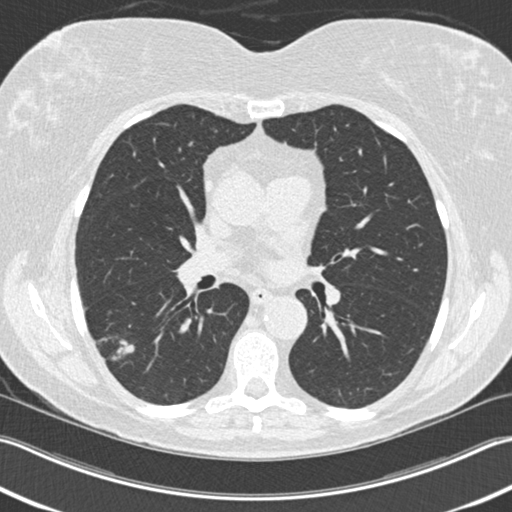
Low-dose screening chest CT, axial slice, baseline annual screen, lung window (W 1500 / L -600 HU), 2 mm slice thickness. Female participant, aged 63 years at enrolment.
- Lesion marked by an expert reader, bounding box <89,322,147,372> (left, top, right, bottom; pixels).
- The screening reader recorded 3 non-calcified nodules or masses ≥4 mm on this exam (right upper lobe, right lower lobe, right lower lobe); which of them this box marks is not recorded.
- Official screen result: positive, change unspecified: nodule(s) >= 4 mm or enlarging nodule(s), mass(es), or other non-specific abnormalities suspicious for lung cancer.
- Participant outcome: lung cancer diagnosed 57 days after this screen — bronchiolo-alveolar adenocarcinoma, NOS, right lower lobe, well differentiated (G1), stage IA (AJCC 6th edition), 25 mm at pathology.